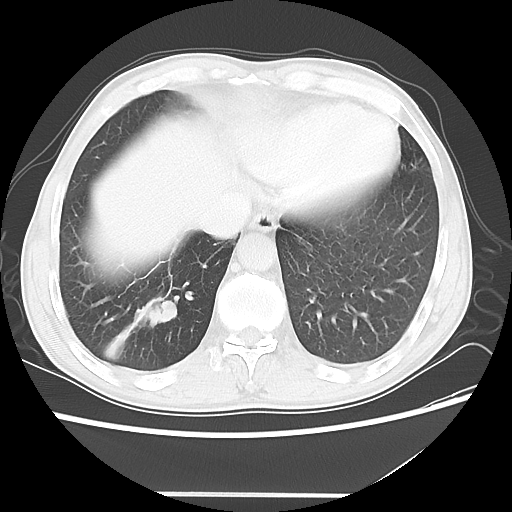
Chest CT, one axial slice; slice 12 of 56 in the series (ordered by position); 120 kVp; lung window (W 1500 / L -600 HU); 512 × 512 image matrix, field of view 344 × 344 mm. Male patient, age 65 years. Case-level facts recorded for this patient, not image findings: clinical TNM (as recorded): T1c N3 M0.
Structures marked on this image (bounding box drawn by a radiologist):
- lung tumour (recorded histology: small cell carcinoma): bounding box <135,287,185,332> (left, top, right, bottom; pixels)